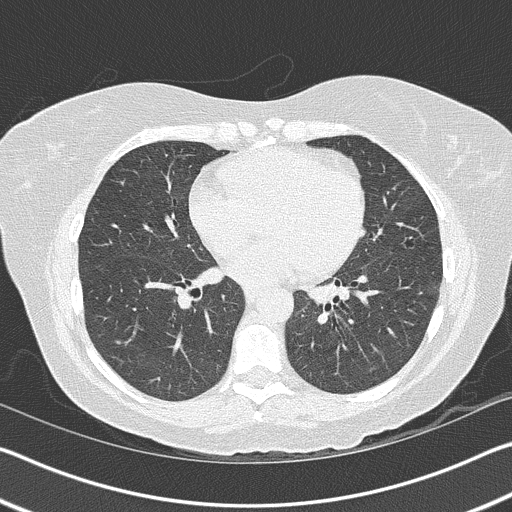
Low-dose screening chest CT, axial slice; first (baseline) screen; lung window (W 1500 / L -600 HU); 120 kVp; slice 73 of 157 in the series; 512 × 512 image matrix, field of view 340 × 340 mm. Female, age 63 years at enrolment. Current smoker at enrolment.
Expert reader's lesion annotation, bounding box [x1, y1, x2, y2] px = [386, 223, 440, 264]. The screening reader recorded 3 non-calcified nodules or masses ≥4 mm on this exam (right upper lobe, left upper lobe, lingula); which of them this box marks is not recorded. Official screen result: positive, change unspecified: nodule(s) >= 4 mm or enlarging nodule(s), mass(es), or other non-specific abnormalities suspicious for lung cancer. Lung cancer was diagnosed 1029 days after this screen (after the third annual screen): bronchiolo-alveolar adenocarcinoma, NOS, lingula, stage IA (AJCC 6th edition), 14 mm at pathology.